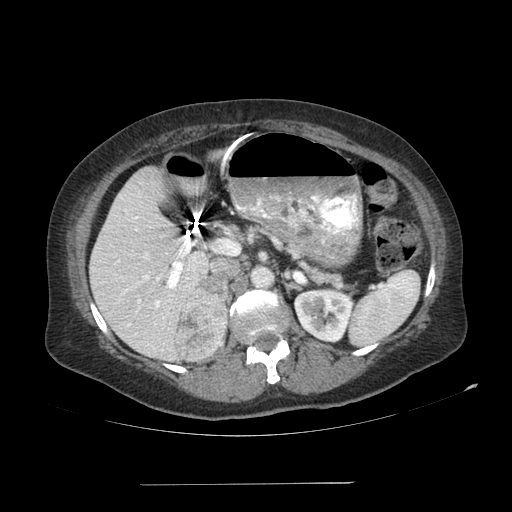
Contrast-enhanced abdominal CT, one axial slice. Position 60 of 113 along the scan axis. 120 kVp. Soft-tissue window (W 400 / L 40 HU). 2.5 mm slice thickness. 512 × 512 image matrix, field of view 440 × 440 mm. Female patient, age 67 years. From the clinical record (not read from this slice): diagnosis: adrenocortical carcinoma; tumour side: right adrenal; tumour size at pathology: 9.8 cm; Ki-67 index: 59 %; stage (as recorded): 4.
Outlined on this slice (semi-automatic segmentation, software-assisted and operator-edited):
- mass: bounding box <177,280,228,360> (left, top, right, bottom; pixels)